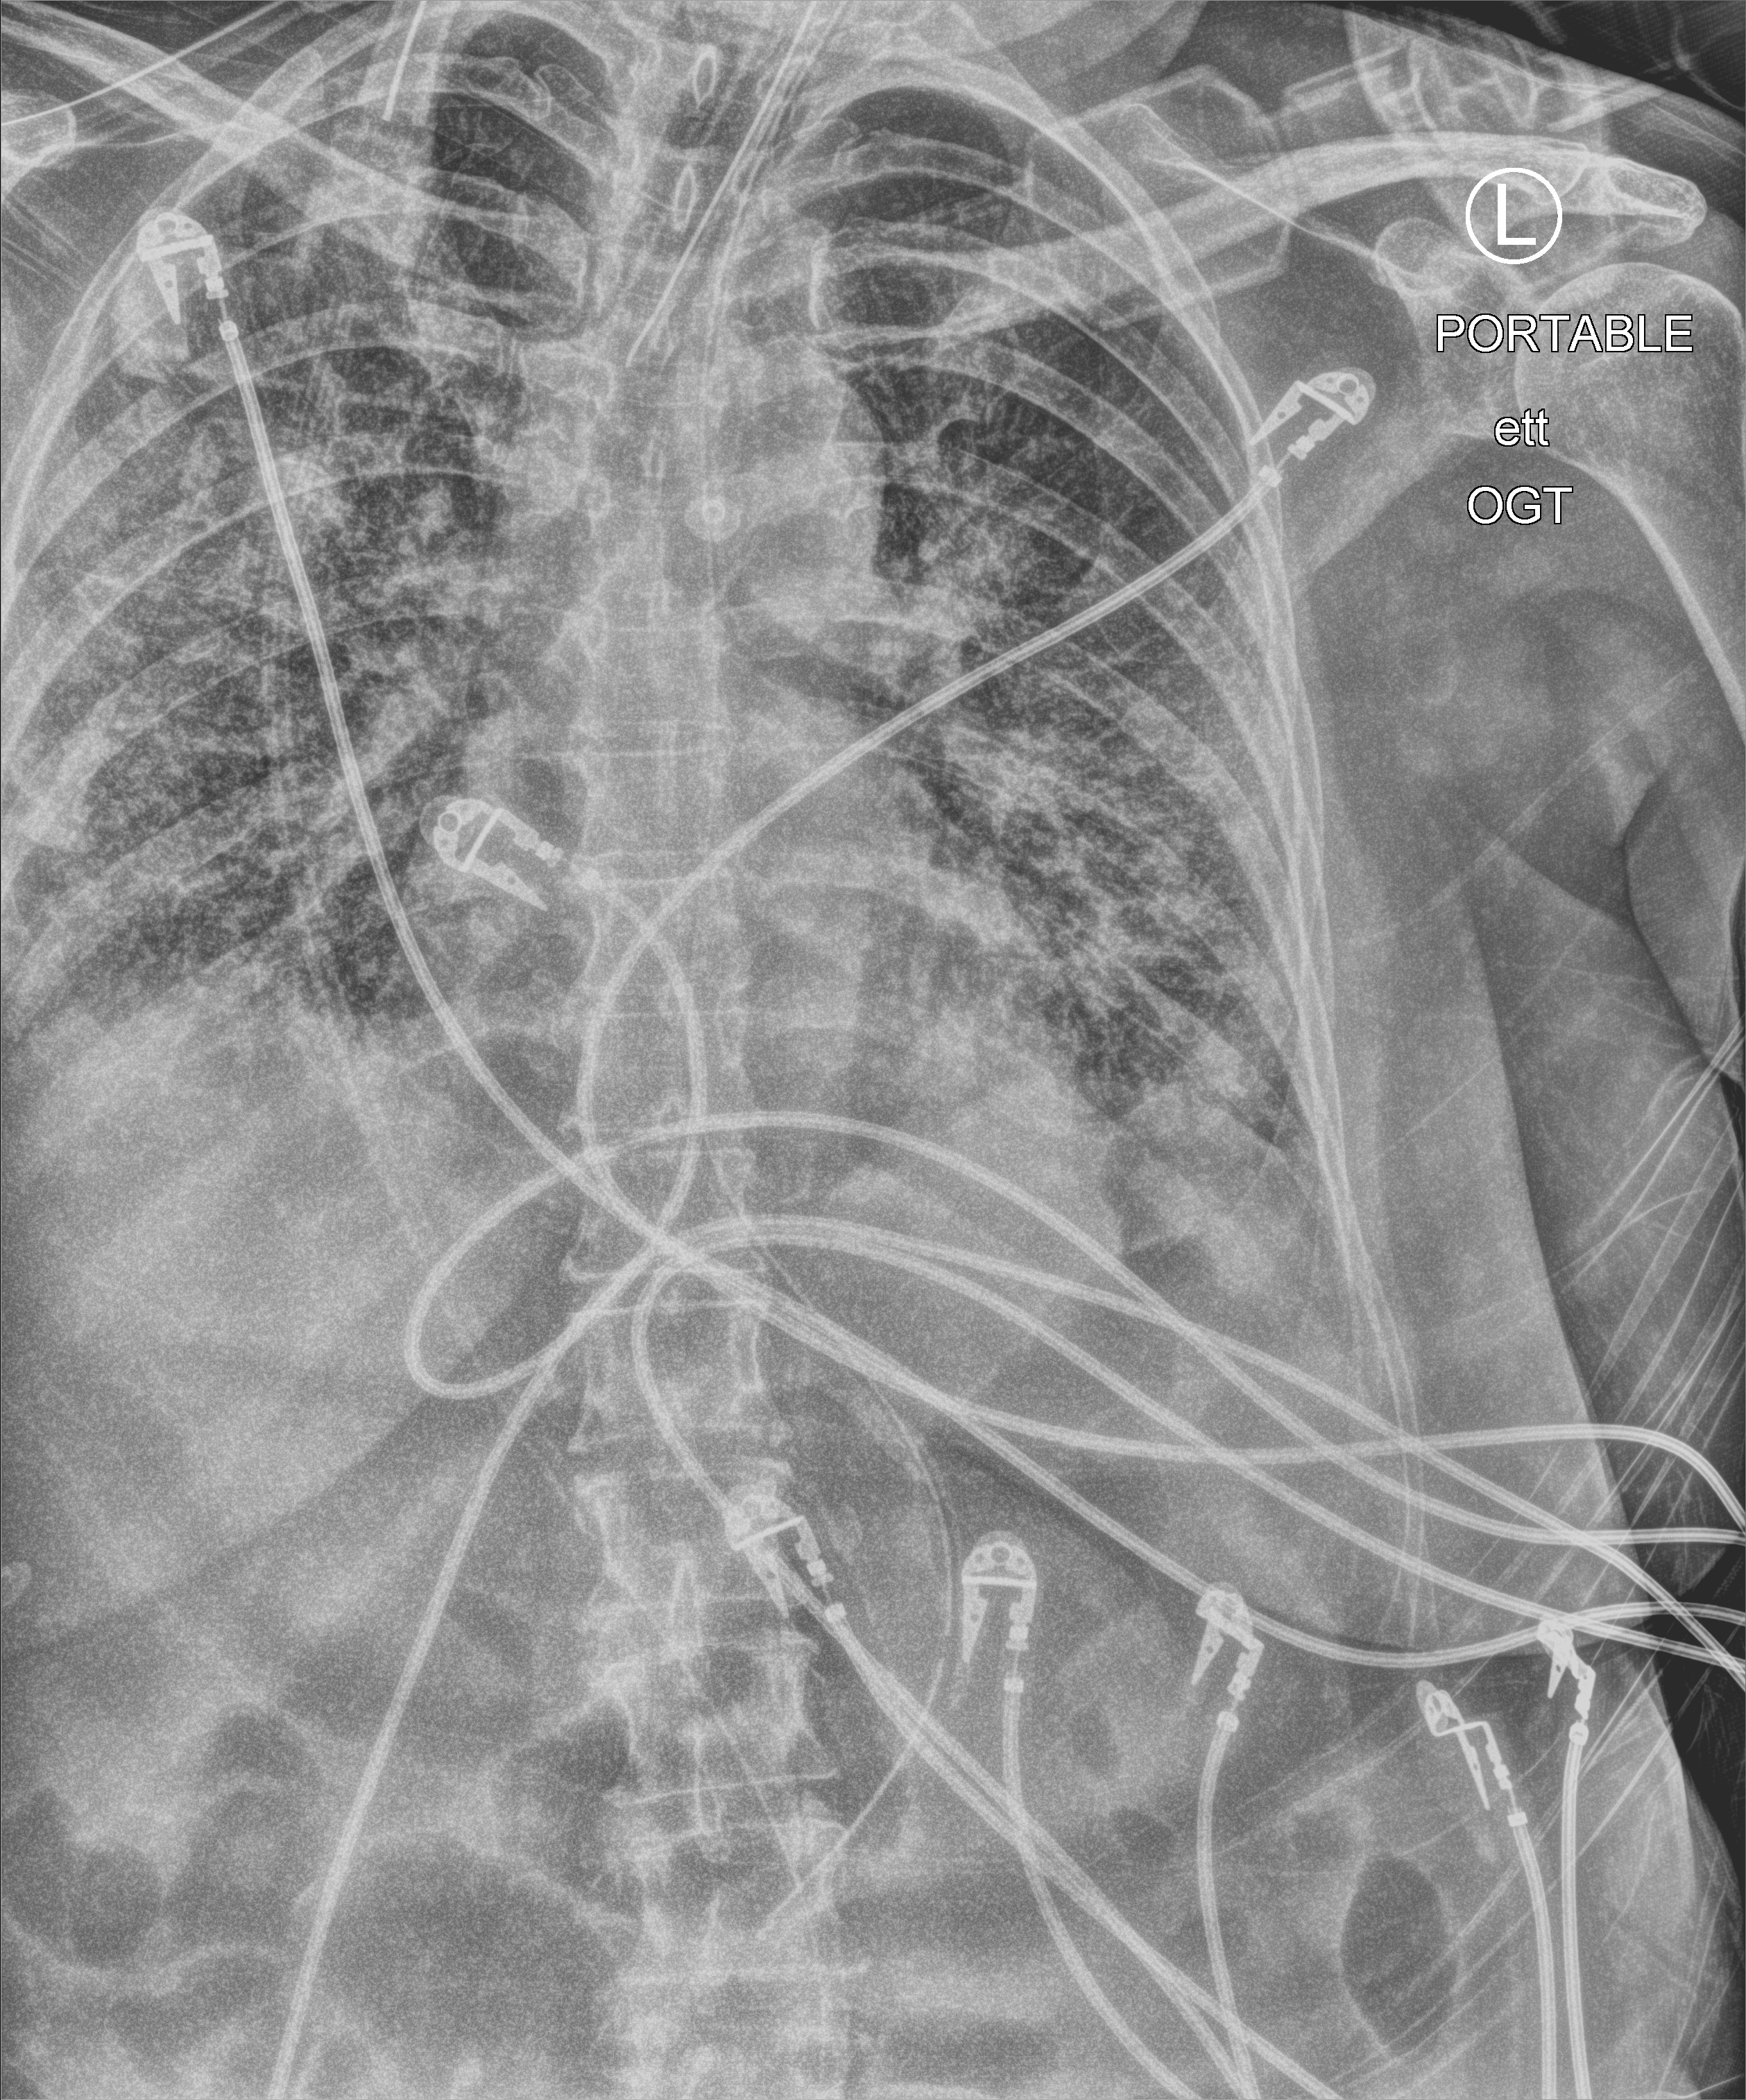
Bedside chest radiograph (computed radiography), anteroposterior (AP) projection. Patient hospitalised with COVID-19; female, aged 60–74 years.
Hospital-stay facts (about this admission, not read from this image; timing relative to this image not recorded):
- chronic kidney disease (admission record): no
- other chronic lung disease (admission record): no
- diabetes (admission record): no